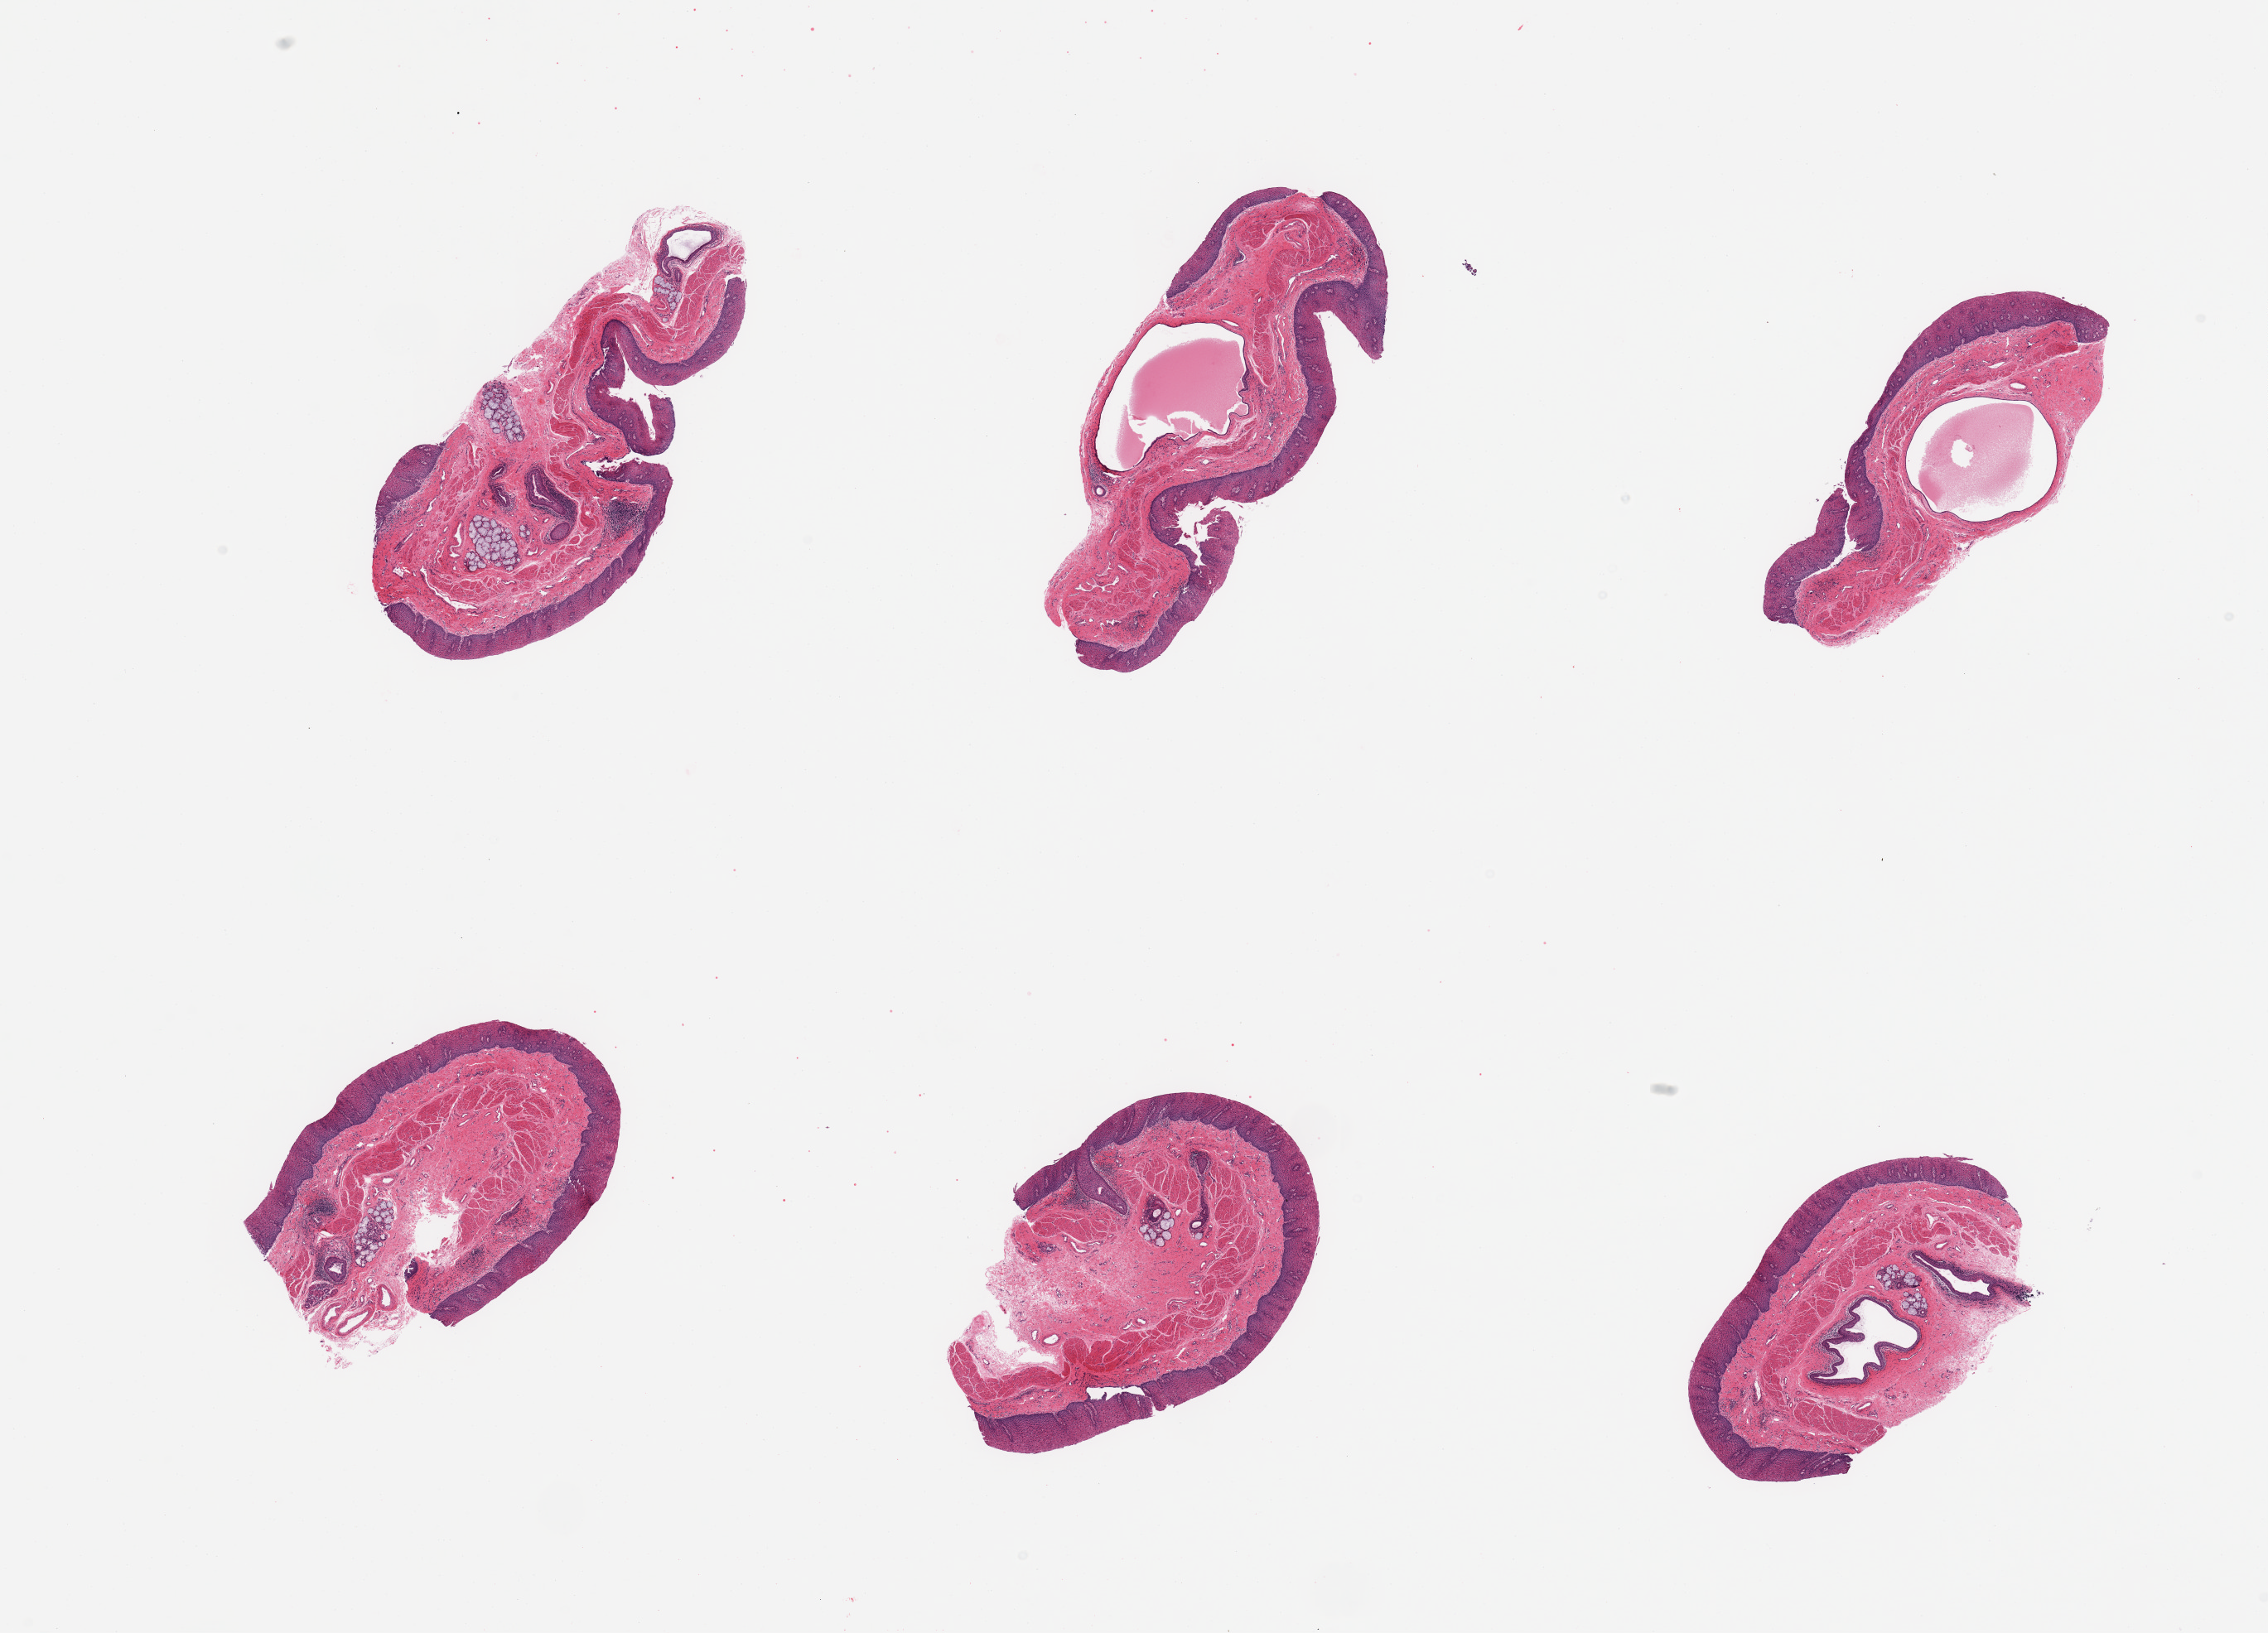
Hematoxylin and eosin (H&E) whole-slide image, whole scanned area (about 21.7 x 15.6 mm, slide scanned at 20x) shown as a low-resolution overview, PAXgene-fixed paraffin-embedded (PFPE) section, target tissue: esophageal mucous membrane, donor tissue sample. Donor sex: female.
Pathologist's review note for this sample: 6 pieces, squamous mucosa up to ~0.3mm, ~10-15% thickness; Submucosal mucuis glands present.